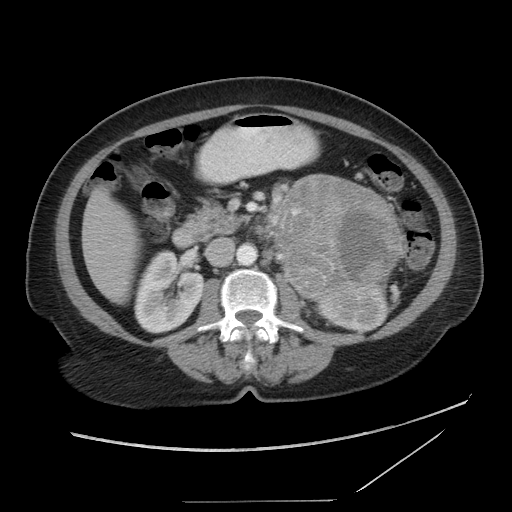
Contrast-enhanced abdominal CT, one axial slice. Slice 48 of 86 in the series (ordered by position). Reconstruction kernel STANDARD. 120 kVp. Intravenous contrast given. Soft-tissue window (W 400 / L 40 HU). 512 × 512 image matrix, field of view 398 × 398 mm. Female patient, age 77 years. Case-level facts recorded for this patient, not image findings: diagnosis: adrenocortical carcinoma; tumour side: left adrenal; tumour size at pathology: 13.1 cm; Ki-67 index: 10 %.
Outlined on this slice (semi-automatic segmentation, software-assisted and operator-edited):
- mass: bounding box <279,177,402,300> (left, top, right, bottom; pixels)